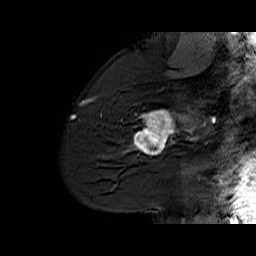
Breast MRI (dynamic contrast-enhanced), one sagittal slice; slice 45 of 60 in the series (ordered by position); dynamic contrast-enhanced series, time point 2 of 6 at this slice position (early post-contrast); 1.5 T; TE 6.1 ms, TR 32.9 ms; 4 mm slice thickness; 256 × 256 image matrix, field of view 220 × 220 mm. Female patient. From the clinical record (not read from this slice): setting: breast cancer imaged before/during neoadjuvant chemotherapy; receptor status: HER2-positive.
Structures marked on this image (semi-automatic segmentation, software-assisted and operator-edited):
- analysis volume of interest (the breast-tissue region the enhancement analysis was run in; not a lesion): box from (x=127, y=95) to (x=194, y=165) px
- tumour enhancement mask (voxels above the 100 % enhancement threshold inside the analysis volume of interest): (x=127, y=109)–(x=194, y=155)